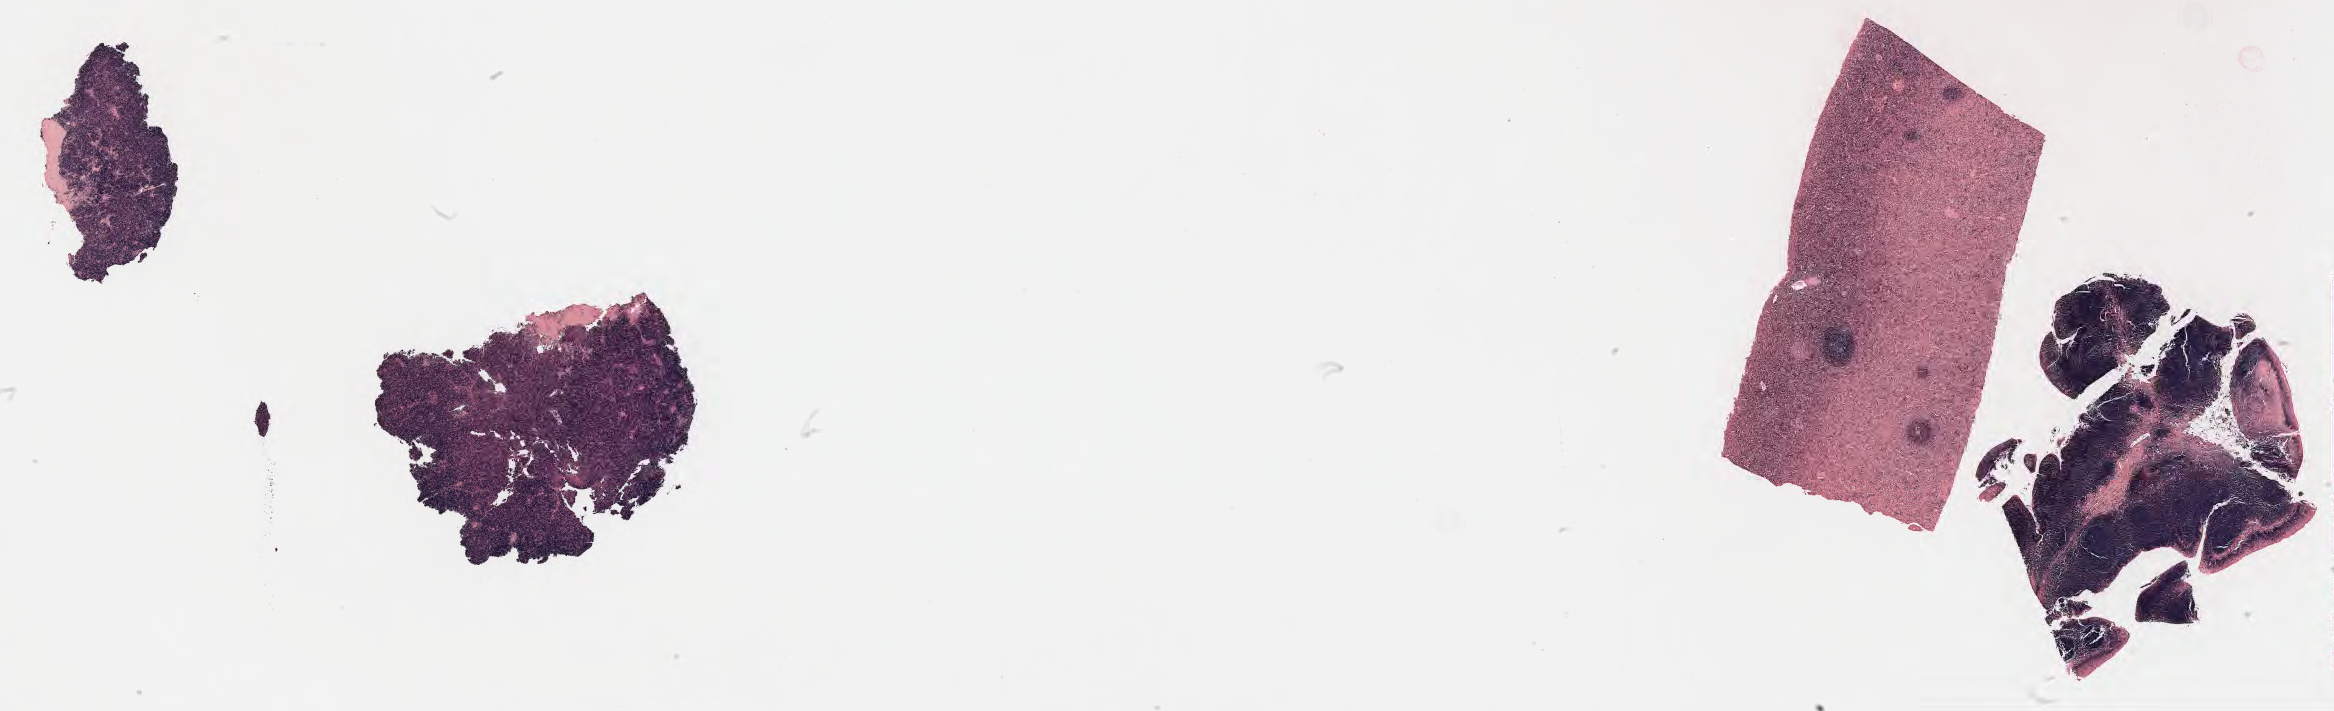
Whole-slide image; stain recorded as Iodonitrotetrazolium, low-resolution overview of the scanned area, about 37.8 x 11.5 mm. Specimen: tumor tissue. Anatomic site: lymph node. Female patient, age 51 years.
Diagnosis: Diffuse large B-cell lymphoma, NOS.